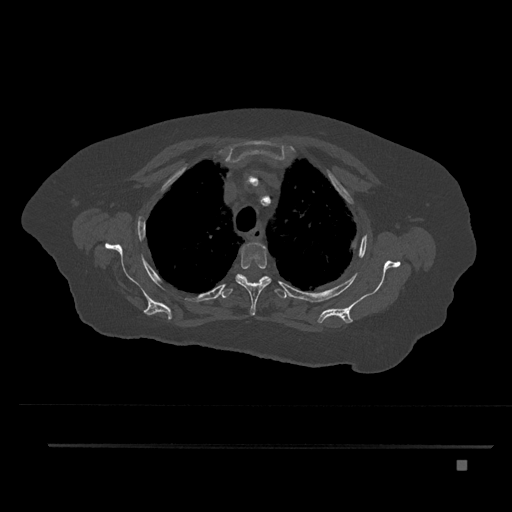
CT including the spine, one axial slice. Position 629 of 797 along the scan axis. Reconstruction kernel Br40s/3. 120 kVp. Bone window (W 1800 / L 400 HU). 0.5 mm slice thickness. 512 × 512 image matrix, field of view 437 × 437 mm. Female patient, age 76 years. From the clinical record (not read from this slice): primary cancer: lung.
Outlined on this slice (semi-automatically segmented with operator editing):
- T3 vertebra: bounding box (x1, y1, x2, y2) in pixels: (235, 242, 271, 316)
- T4 vertebra: (221, 274, 287, 299)